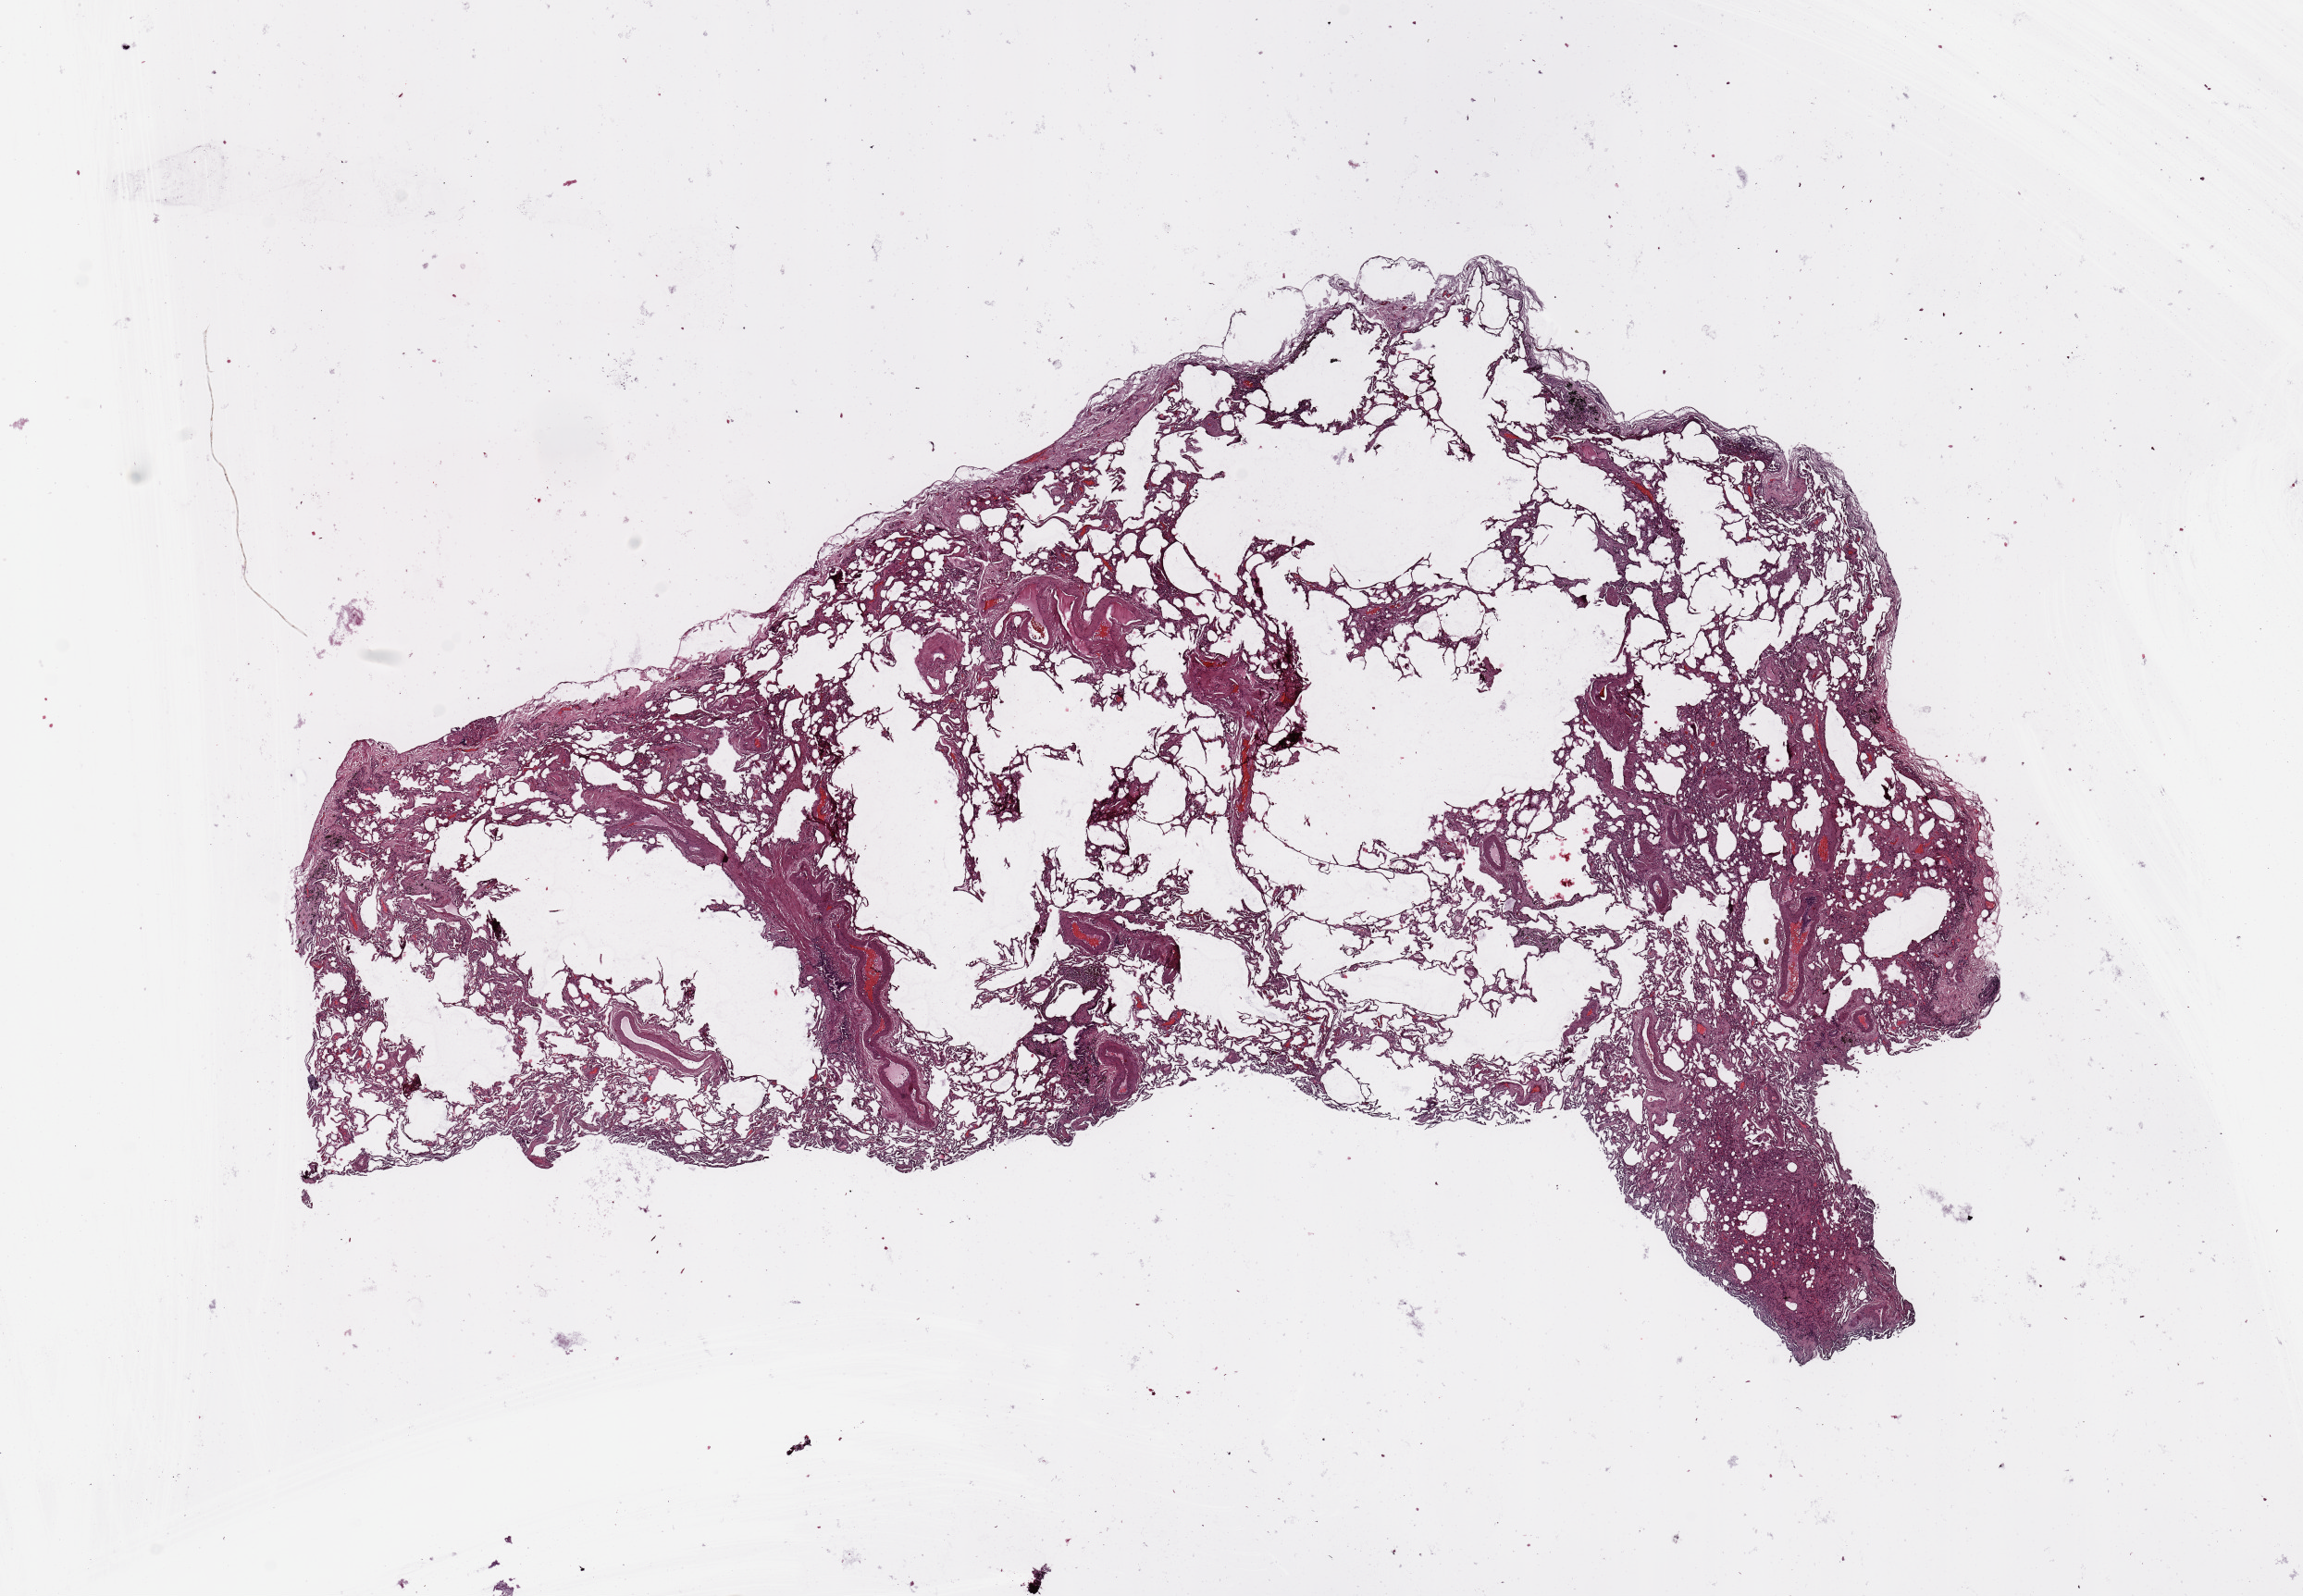
Digitized H&E-stained tissue section (whole slide), shown as a low-resolution overview of the whole scanned area (about 19.7 x 13.6 mm); normal (non-tumour) tissue sample, sampled site: lung. Male, 66 y/o.
• this section: normal (non-tumour) tissue from the same patient
• patient diagnosis: Squamous cell carcinoma, NOS